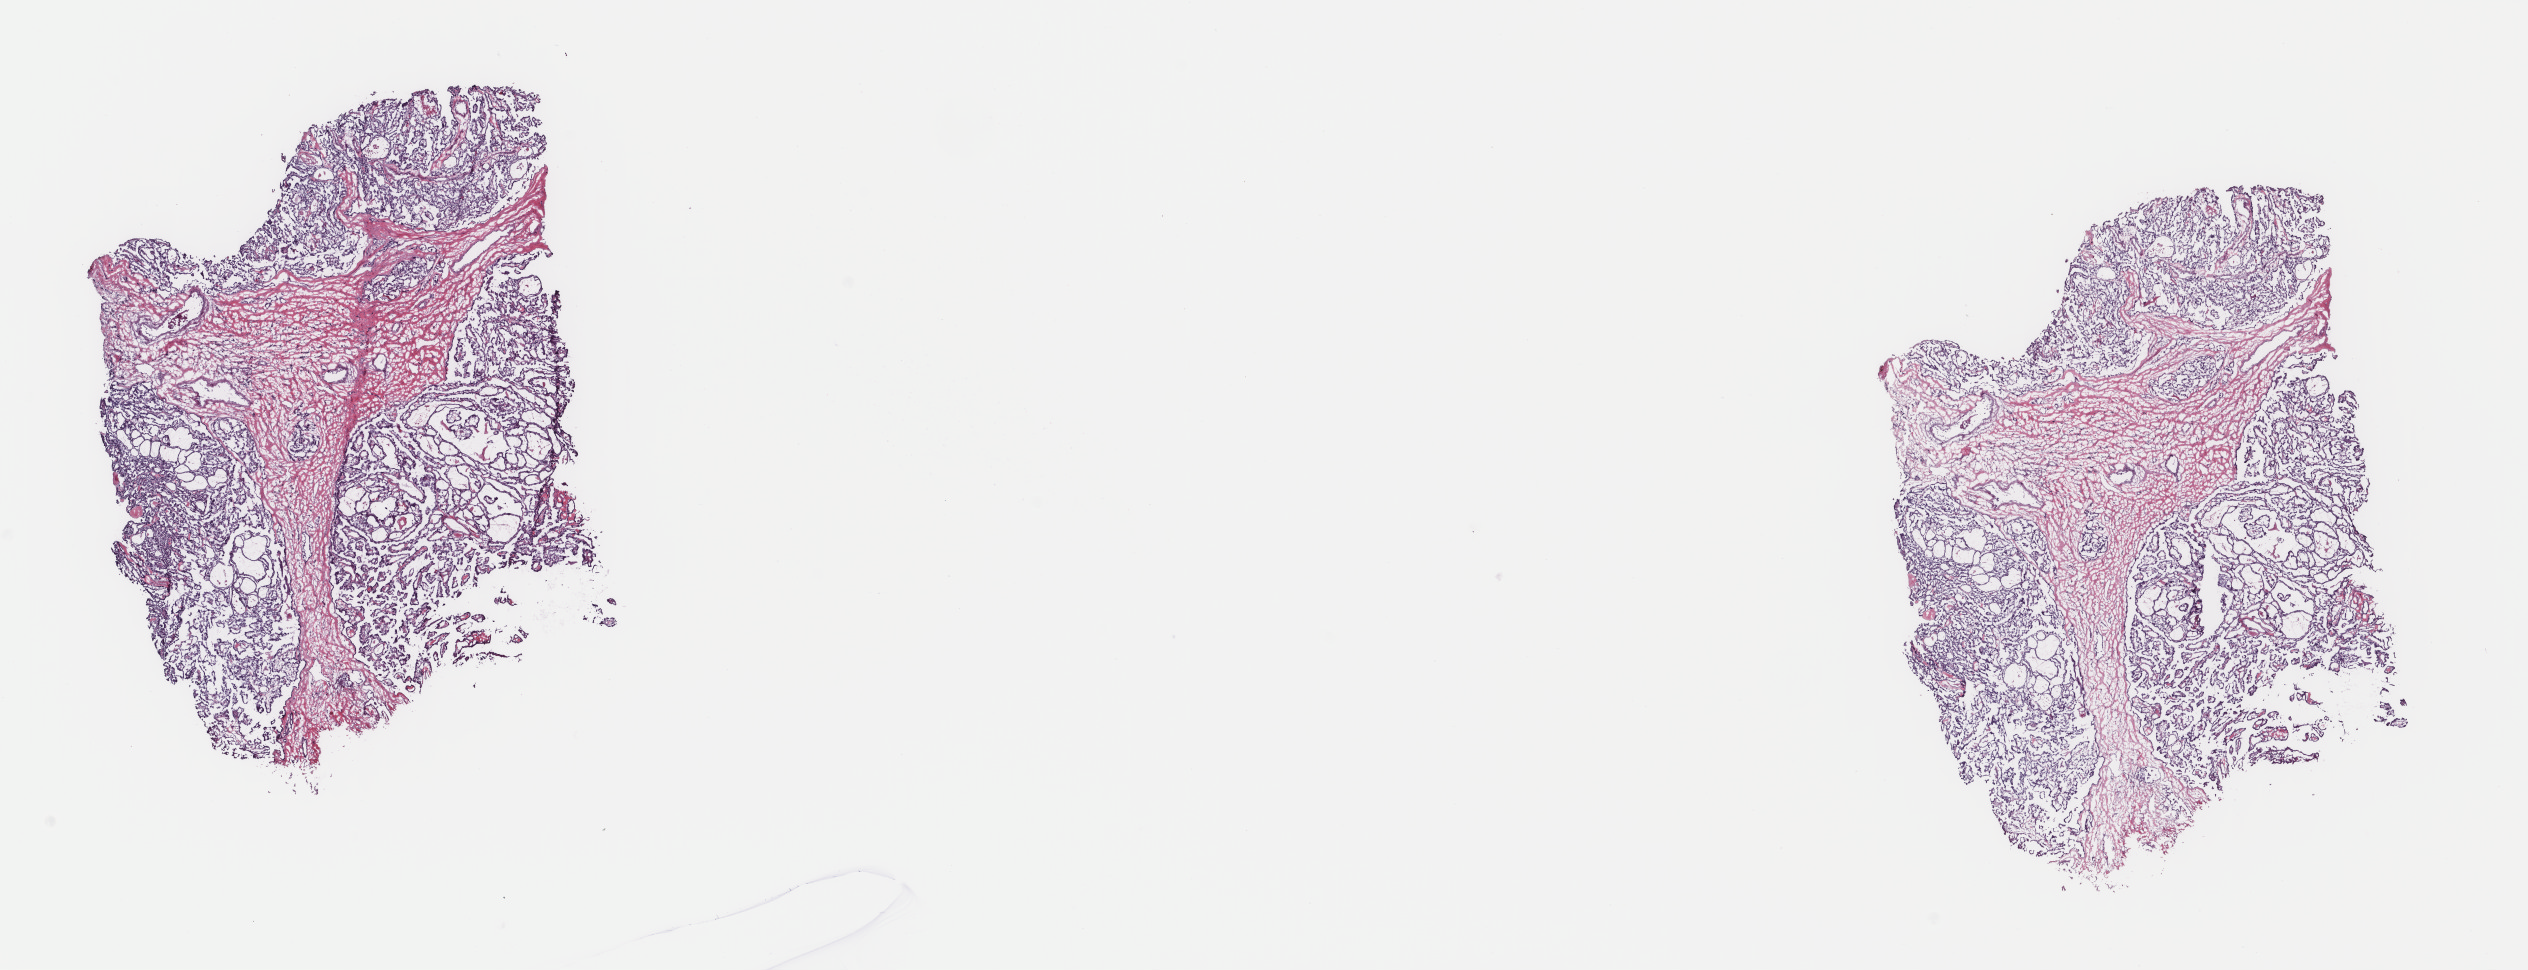
Digitized H&E tissue section (whole slide), low-resolution overview of the scanned area, about 20.1 x 7.7 mm (from a 40x scan); frozen section from the top of the tissue portion; sample: primary tumour, thyroid. Patient: female, age at initial diagnosis 49 years. Slide review estimates, as recorded: tumour cells 90%, tumour nuclei 85%, normal cells 0%, stromal cells 10%, necrosis 0%. Inflammatory infiltration, as recorded: lymphocyte infiltration 0%, monocyte infiltration 0%, neutrophil infiltration 0%.
Laterality: right. Histologic diagnosis: Papillary adenocarcinoma, NOS. AJCC pathologic stage: II (7th edition).